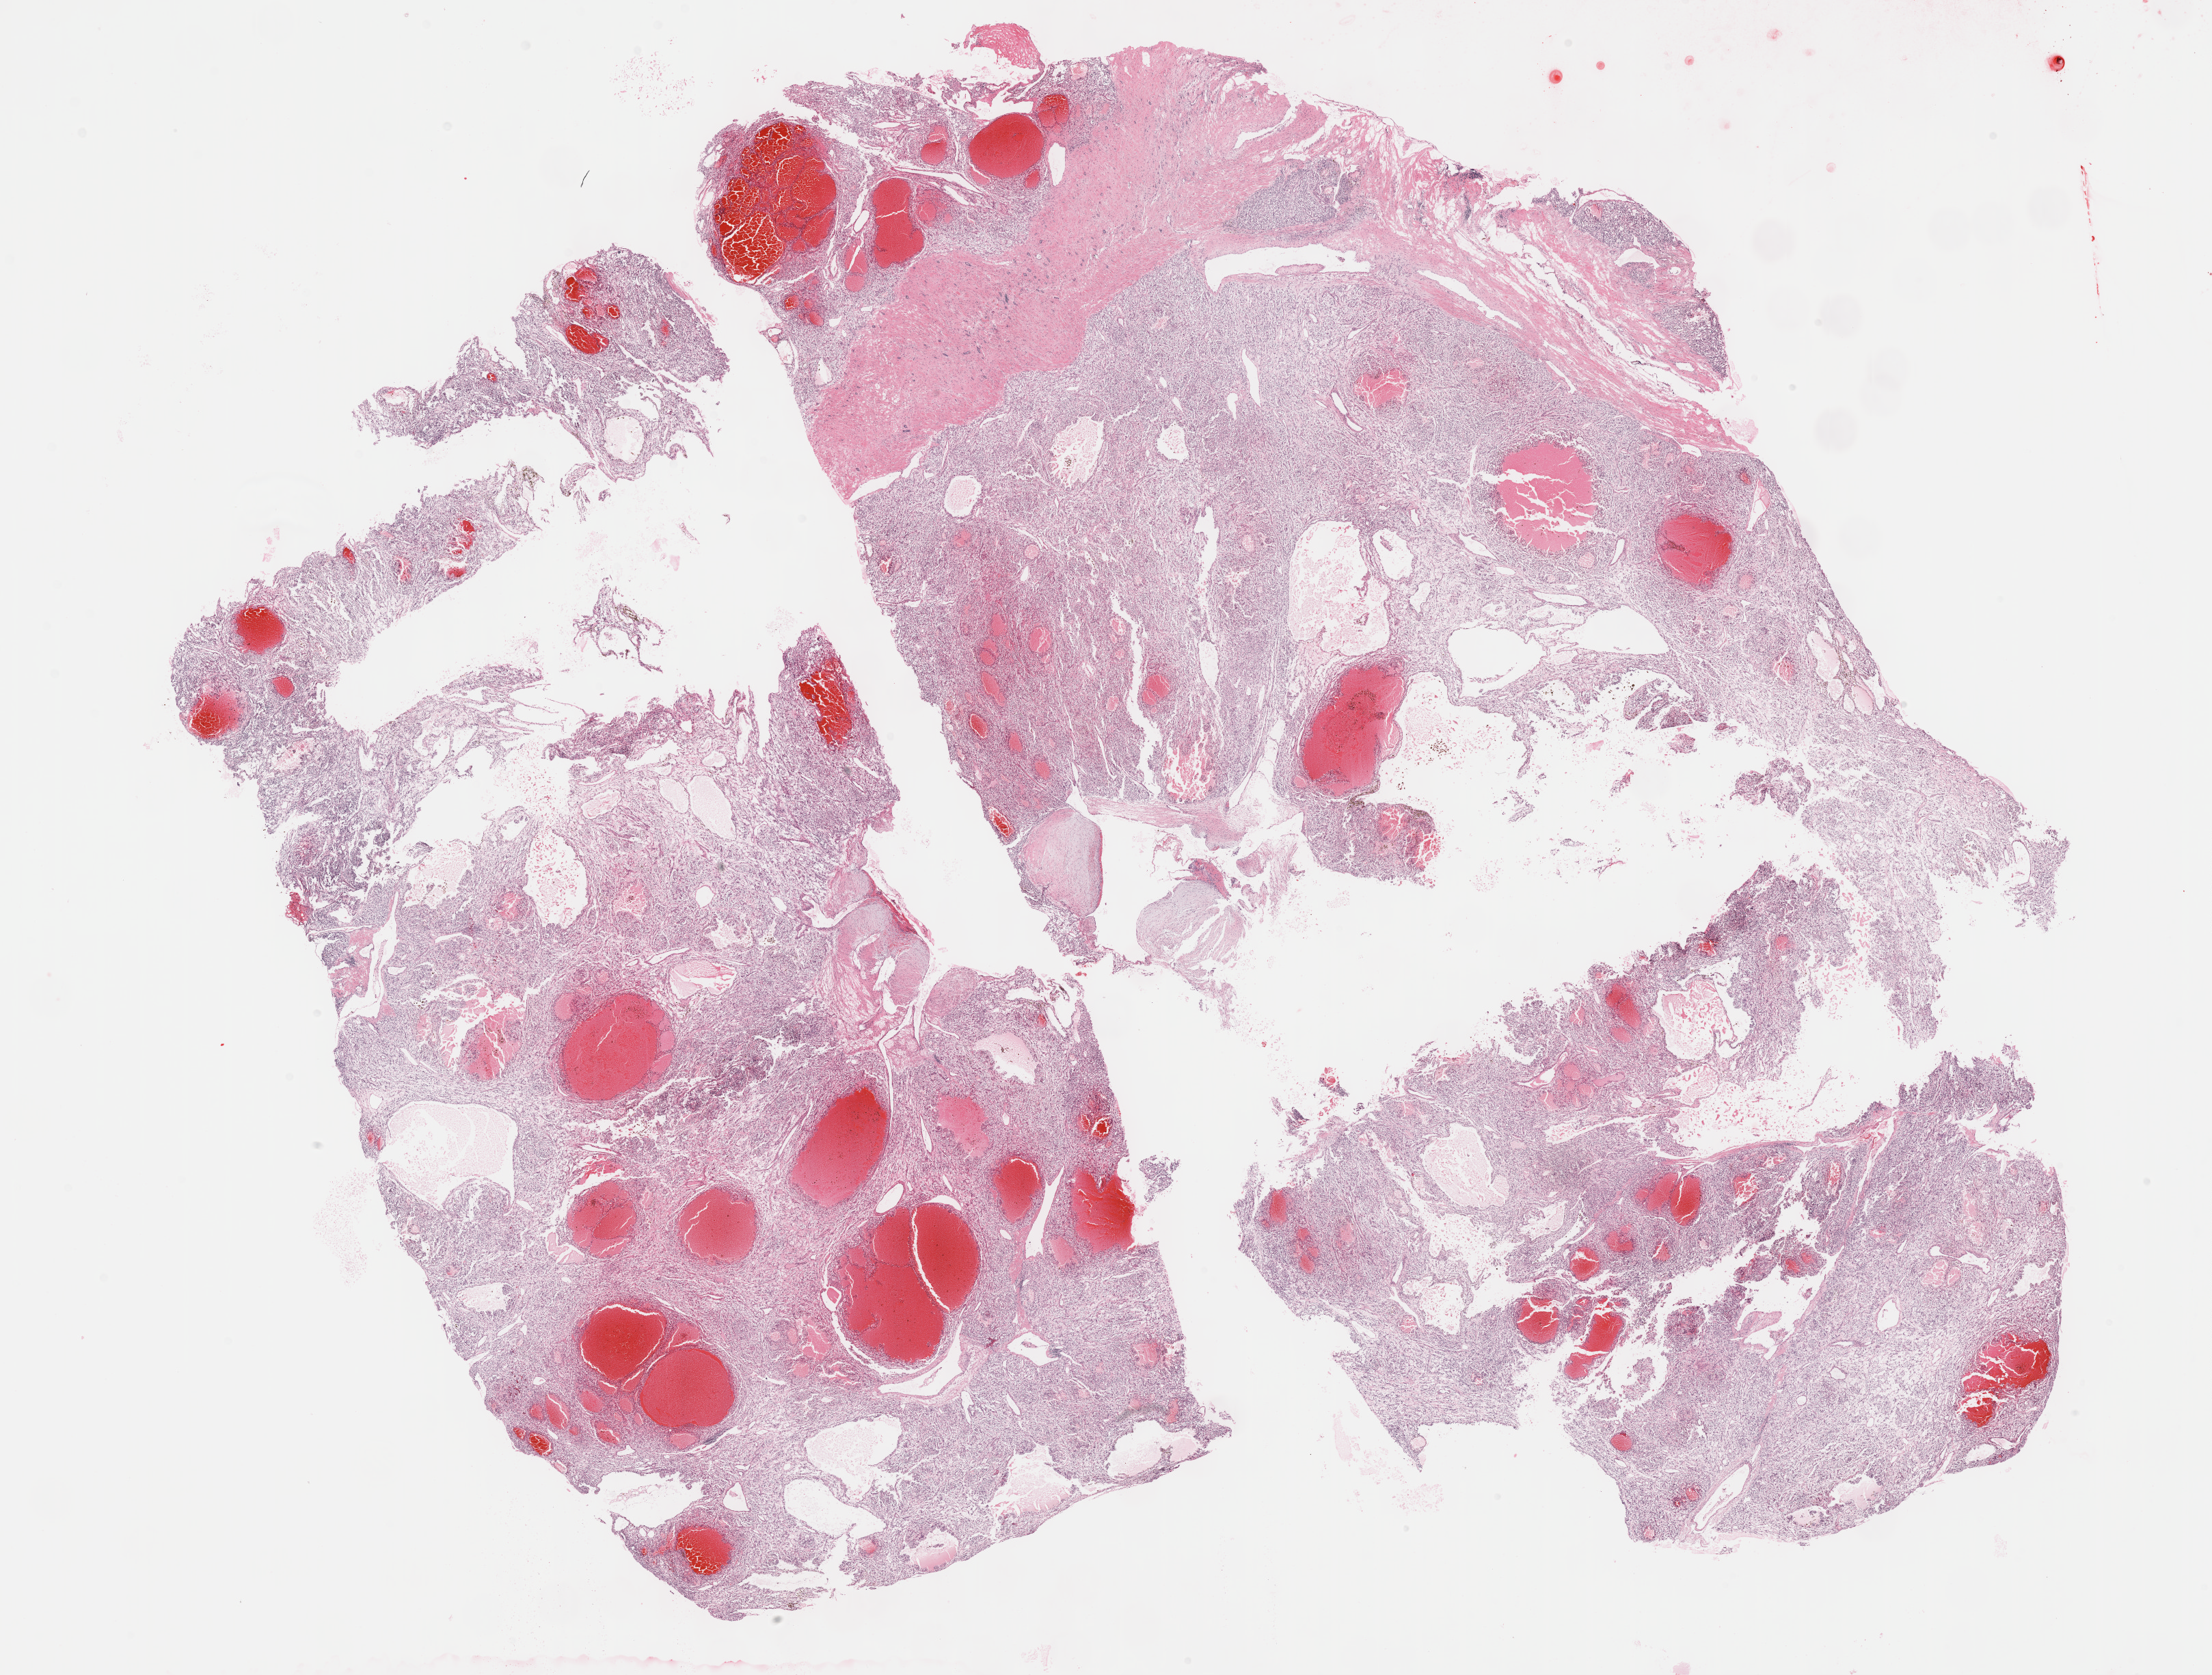
Digitized H&E-stained tissue section (whole slide) — shown as a low-resolution overview of the whole scanned area (about 26.2 x 19.8 mm); FFPE section; primary tumour sample from the kidney. Patient: female, age at initial diagnosis 62 years.
Diagnosis: Clear cell adenocarcinoma, NOS.